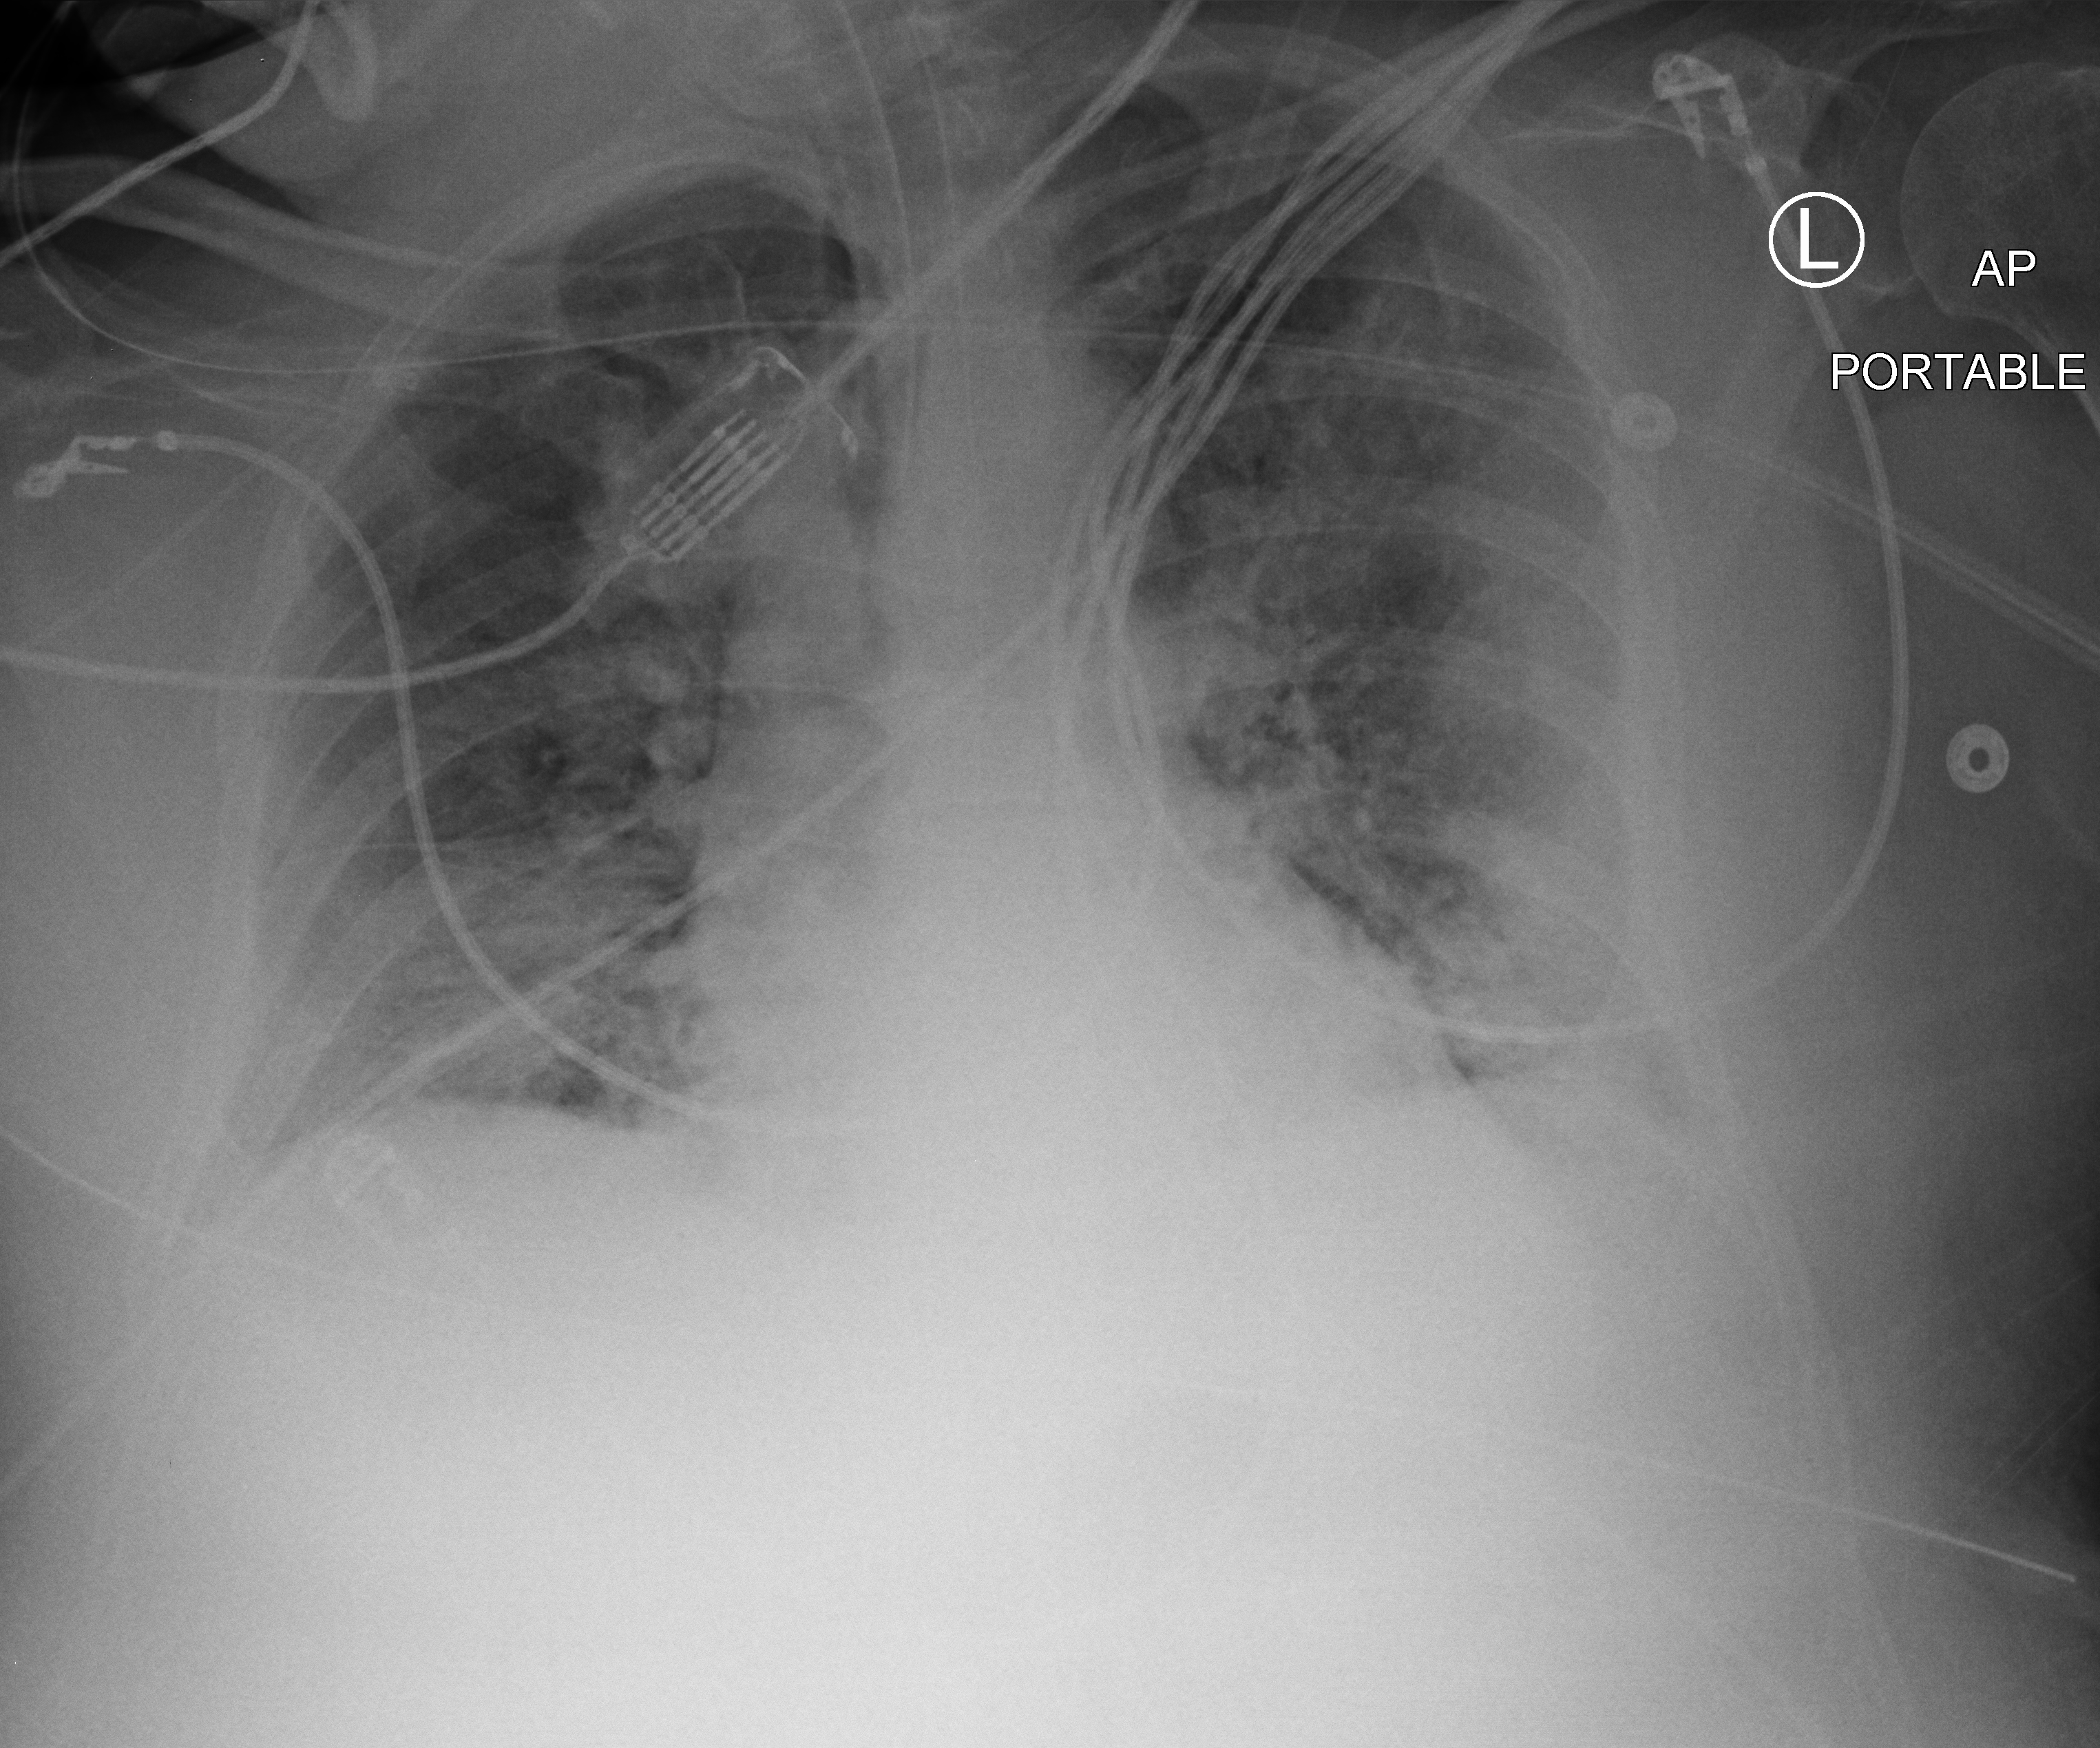
Bedside chest radiograph (computed radiography). Patient hospitalised with COVID-19; male, aged 60–74 years.
From the hospital-stay record, not from the radiograph (when in the stay this image was taken is not recorded): mechanically ventilated during this hospital stay: yes.